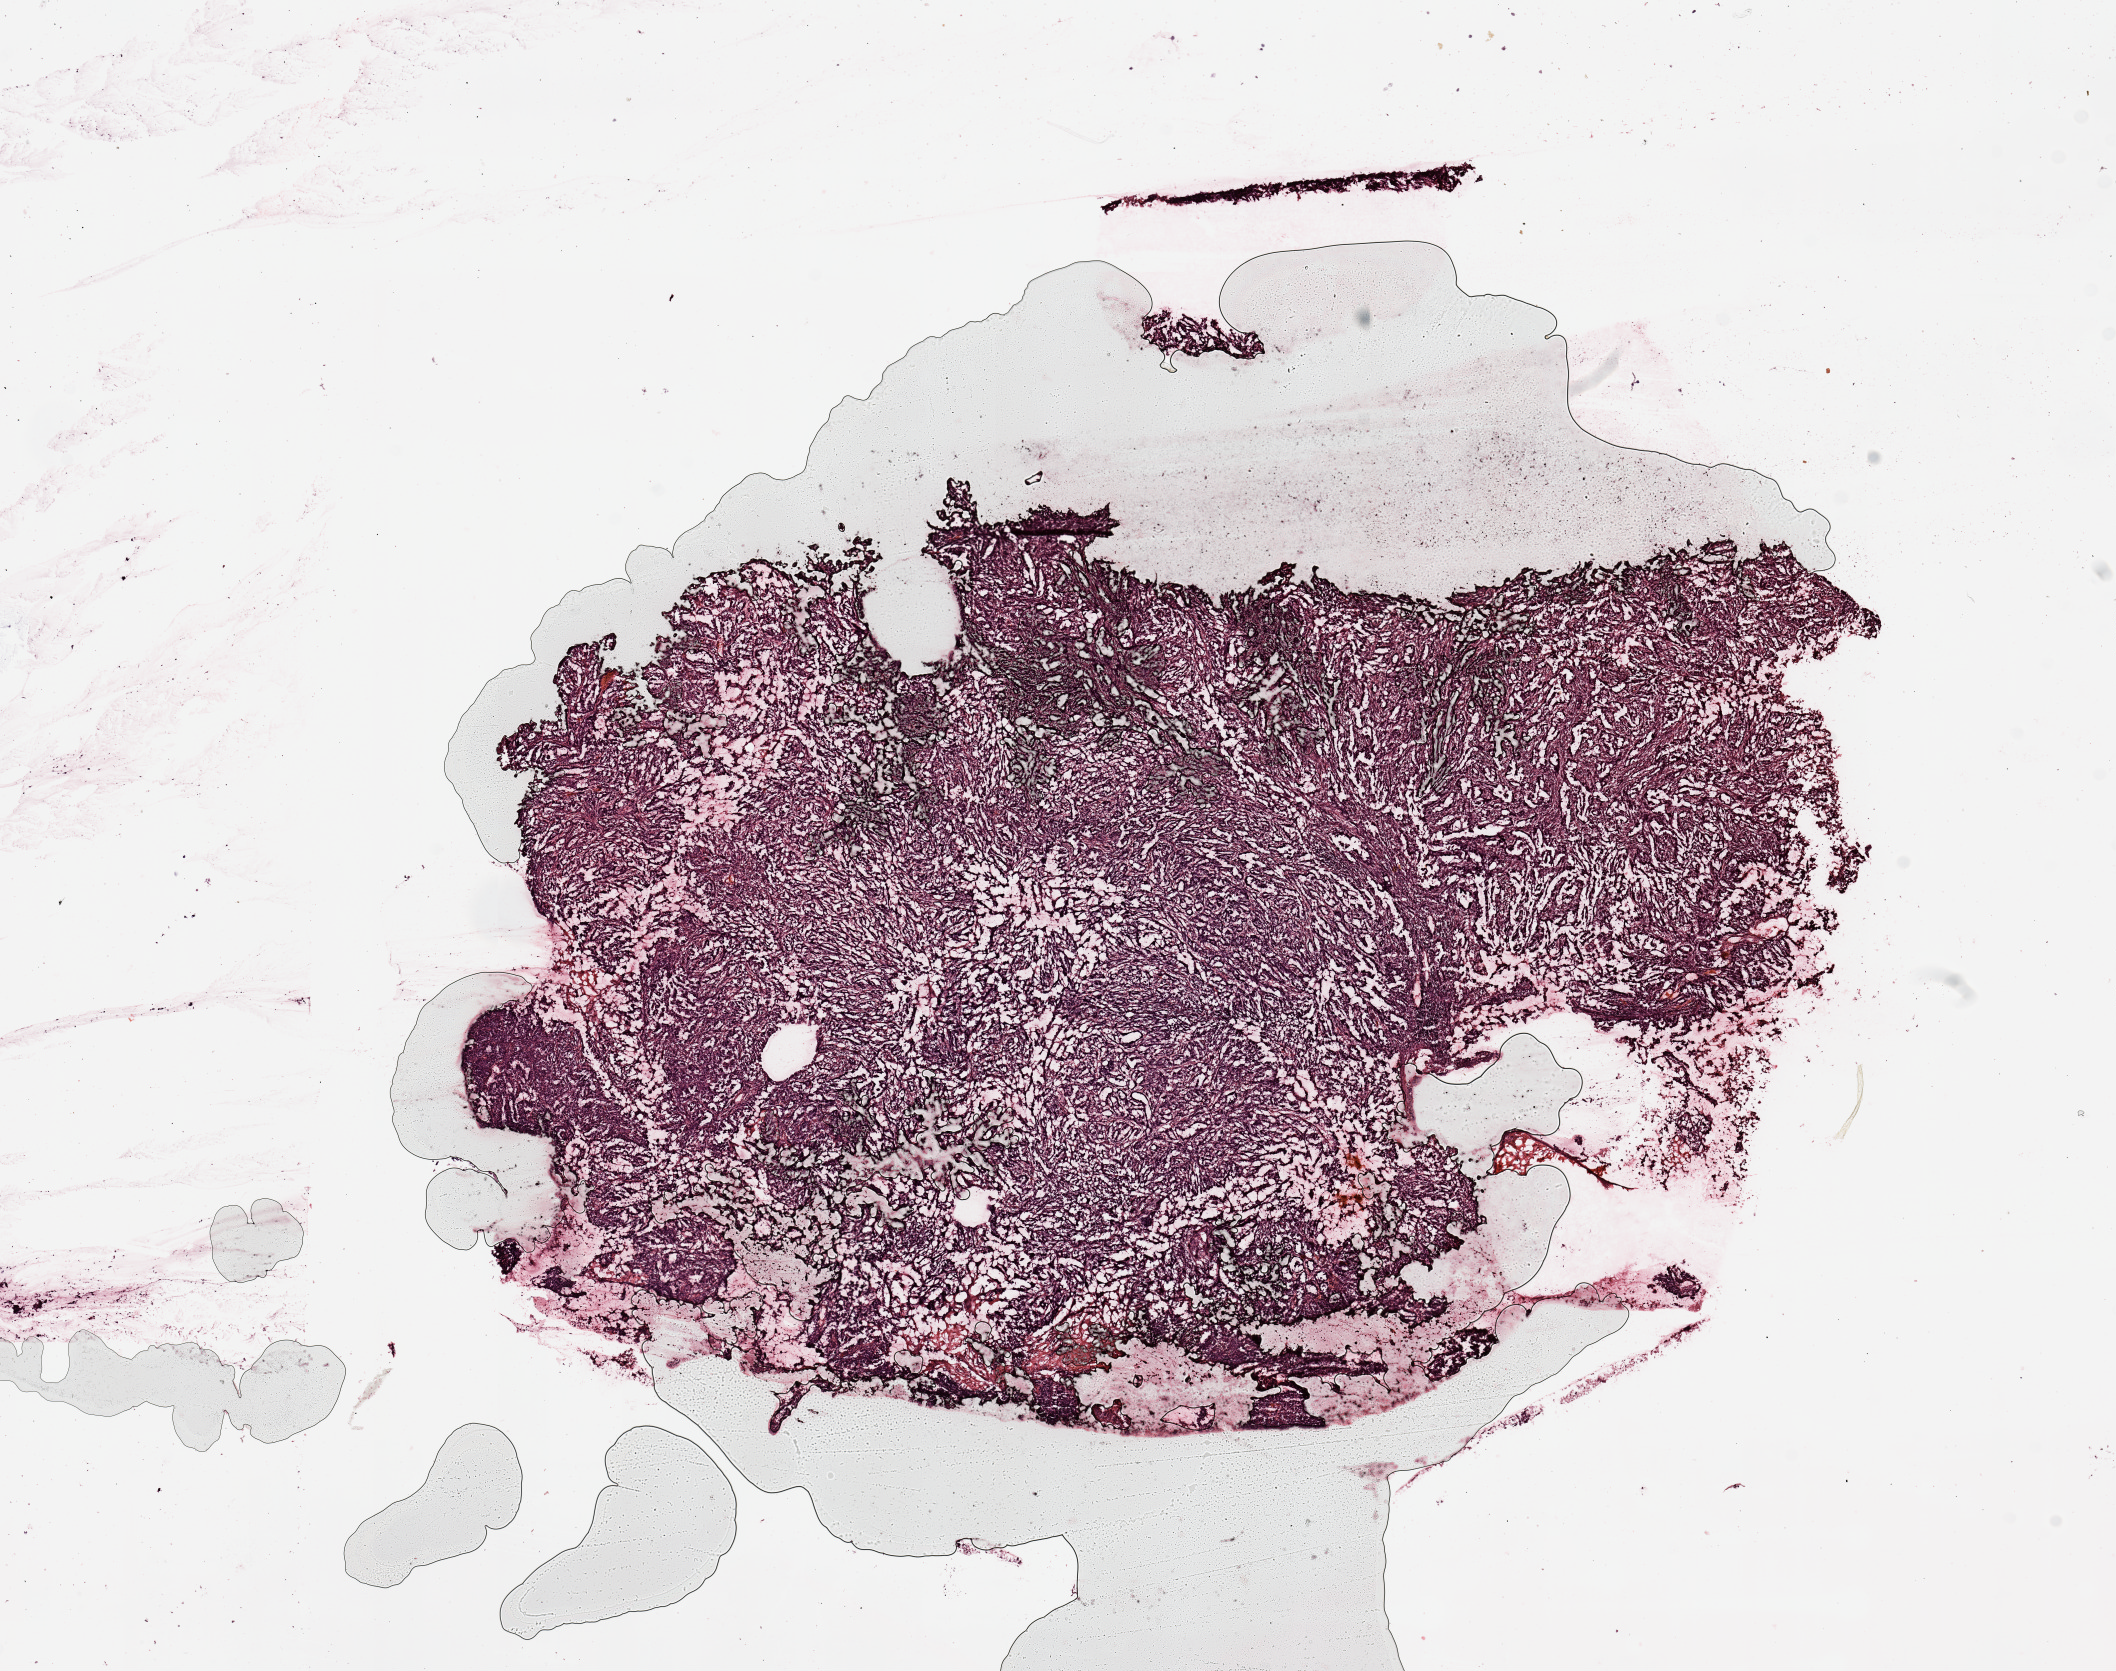
Hematoxylin and eosin (H&E) stained whole-slide image, a low-resolution overview of the entire scanned area, about 16.7 x 13.2 mm (acquisition: 20x scan). Tumour tissue sample, sampled site: uterus. Patient: female, age 57 years. Histologic grade: G3 (poorly differentiated). Pathologist review of this section (percent, as recorded): tumour nuclei 95%, necrosis 5%.
* AJCC pathologic stage: I
* histologic diagnosis: Endometrioid adenocarcinoma, NOS